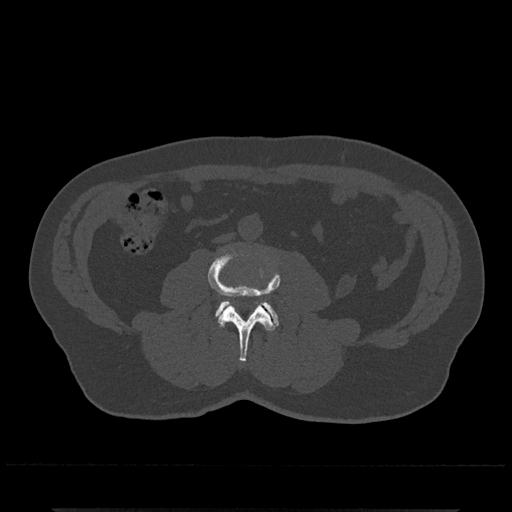
CT including the spine, one axial slice. Position 204 of 797 along the scan axis. Bone window (W 1800 / L 400 HU). 0.5 mm slice thickness. 512 × 512 image matrix, field of view 393 × 393 mm. Male patient, age 67 years. Case-level facts recorded for this patient, not image findings: primary cancer: prostate.
Outlined on this slice (semi-automatically segmented with operator editing):
- L3 vertebra: bounding box [x1, y1, x2, y2] px = [208, 251, 281, 362]
- L4 vertebra: [216, 300, 279, 326]